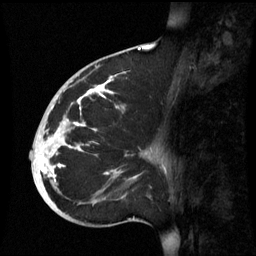
Breast MRI (dynamic contrast-enhanced), one sagittal slice; position 29 of 60 along the scan axis; dynamic contrast-enhanced series, image 2 of 3 at this slice position (ordered by acquisition); 1.5 T; TE 4.2 ms, TR 8.9 ms; 2.6 mm slice thickness; 256 × 256 image matrix, field of view 220 × 220 mm. Patient: female, 35 years. Case-level facts recorded for this patient, not image findings: setting: breast cancer imaged before/during neoadjuvant chemotherapy; receptor status: HR-positive, HER2-negative.
Annotated regions visible in this slice (semi-automatically segmented with operator editing):
- analysis volume of interest (the breast-tissue region the enhancement analysis was run in; not a lesion): bounding box (x1, y1, x2, y2) in pixels: (32, 74, 164, 221)
- tumour enhancement mask (voxels above the 70 % enhancement threshold inside the analysis volume of interest): (39, 76, 116, 183)